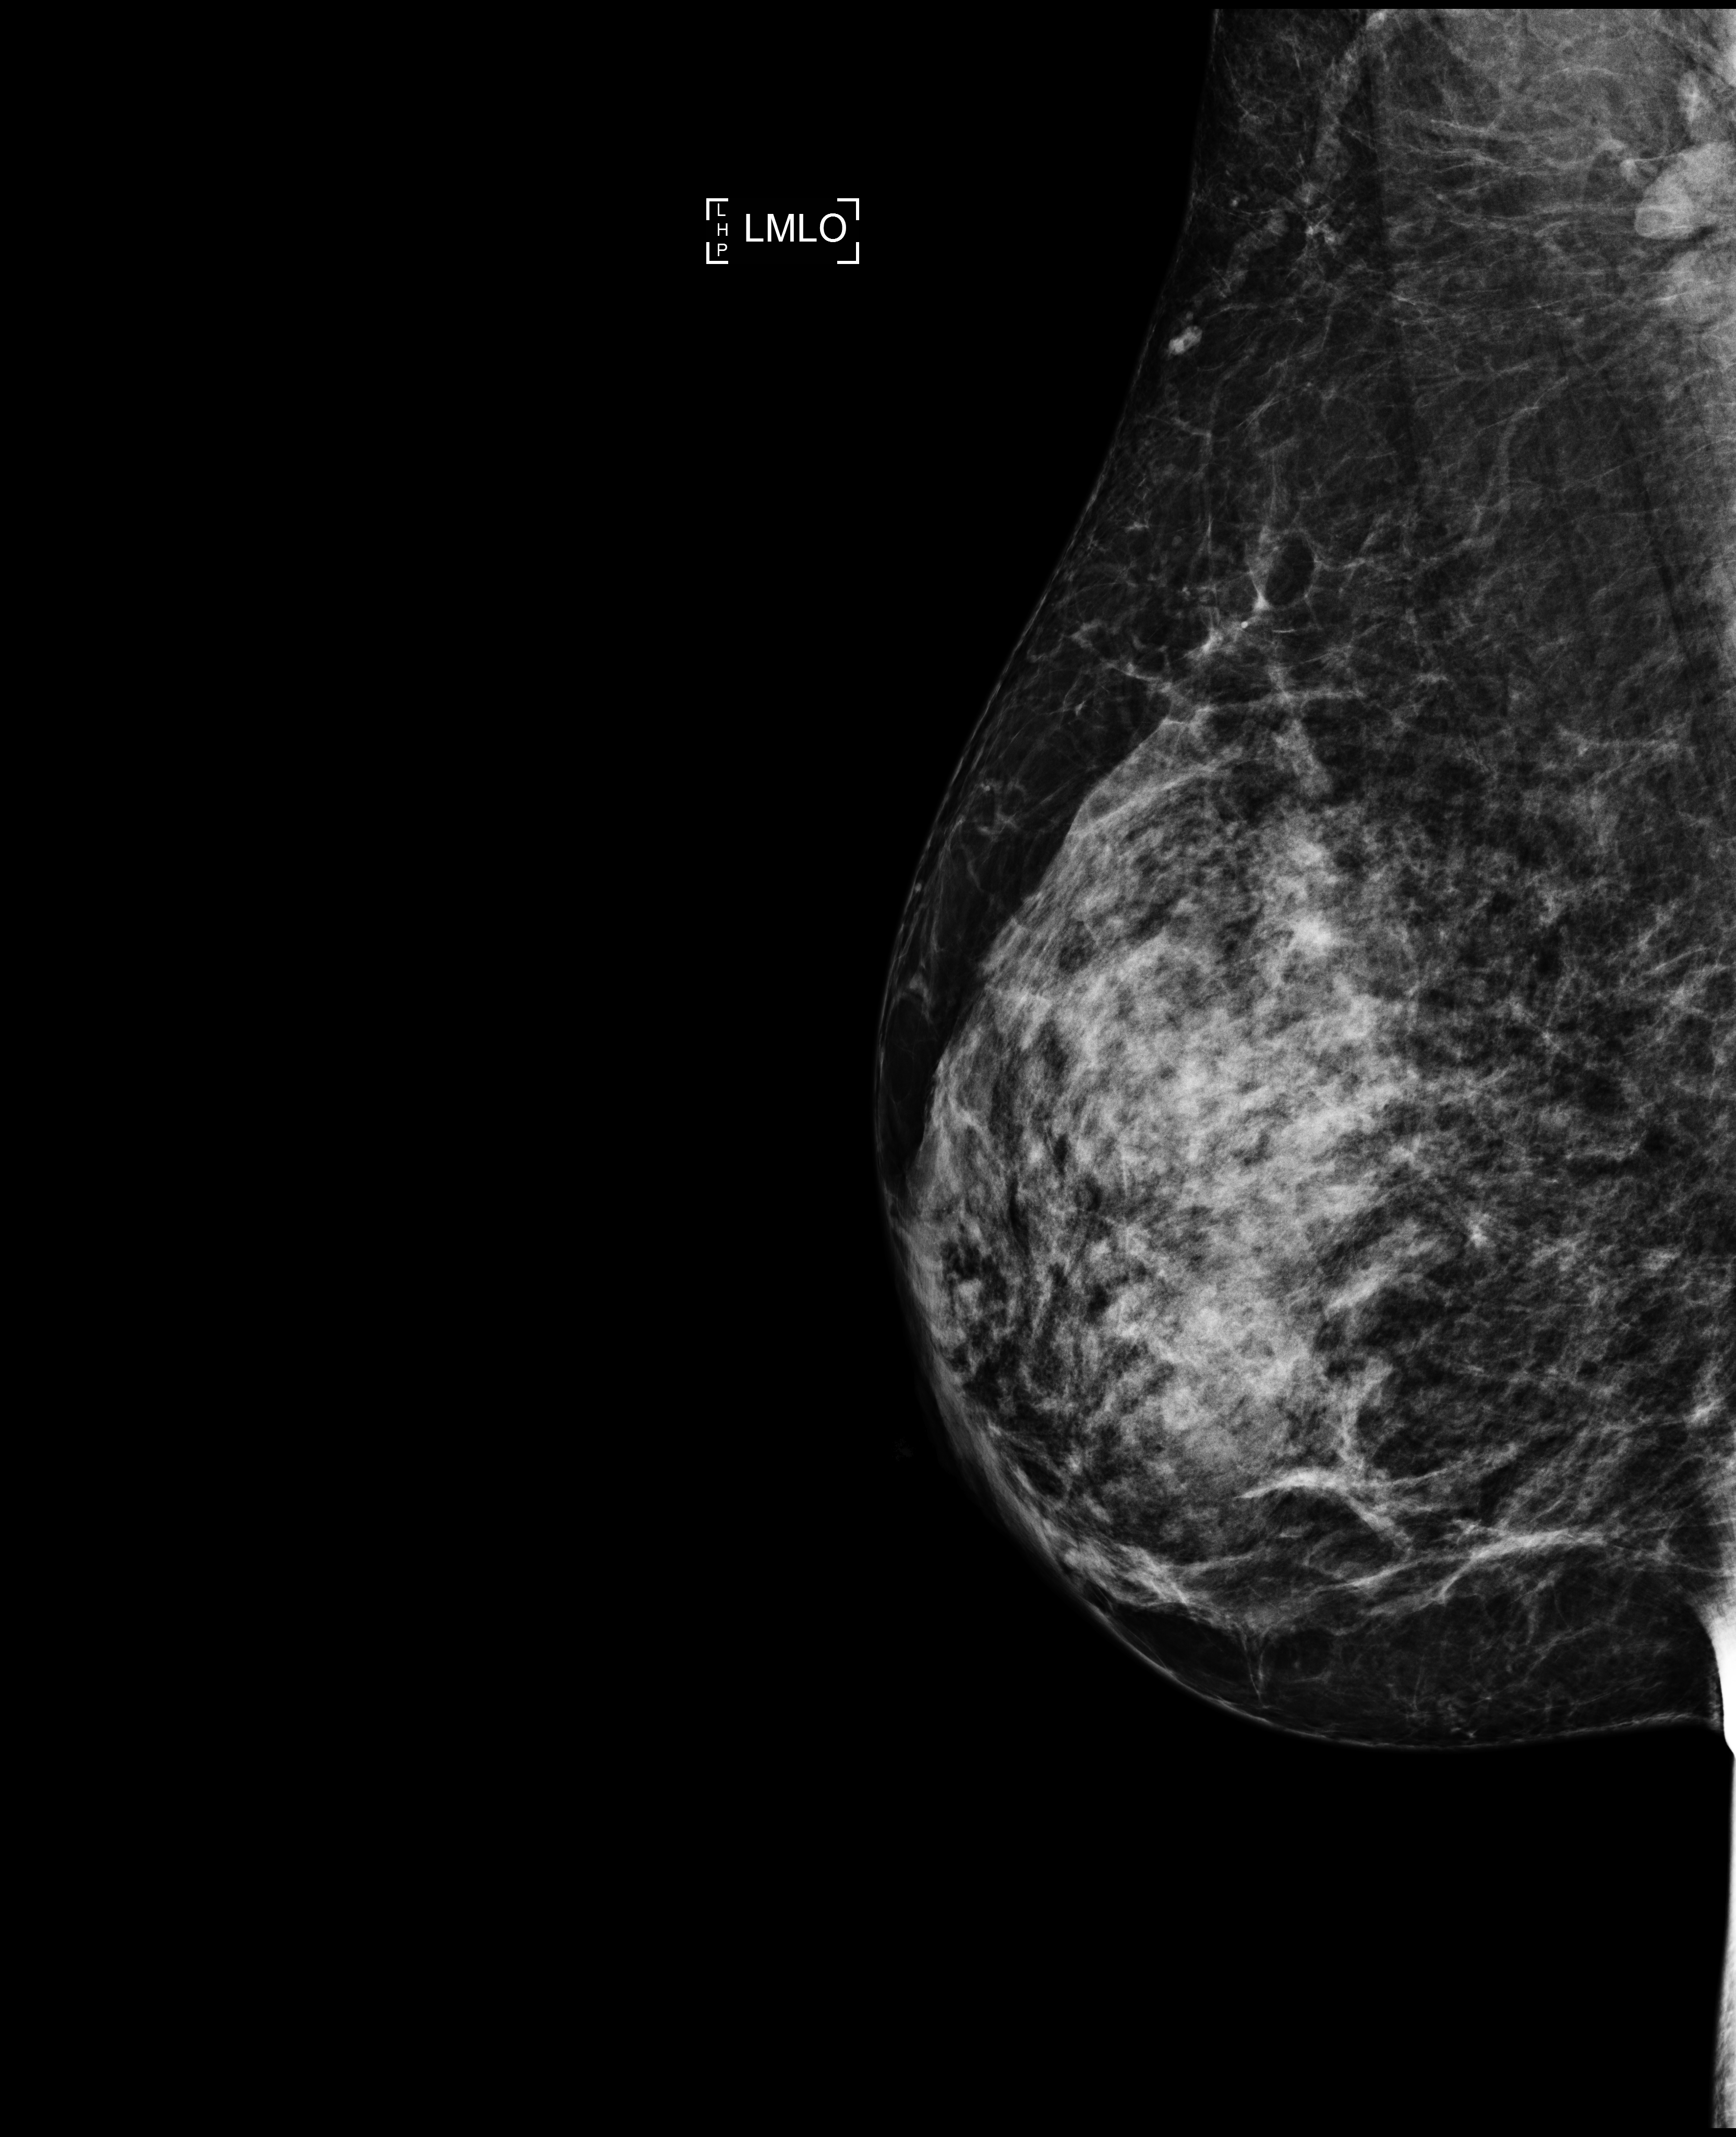
Annual screening mammography examination. Patient aged 42 years (female).
Image type: full-field digital mammogram. Breast: left. Projection: medio-lateral oblique projection. BI-RADS breast density category at the screening exam (both breasts, scale 1–4): 3. Final BI-RADS assessment for this screening round (tomosynthesis exam, both breasts): category 1. Recall: no recall after this screen.